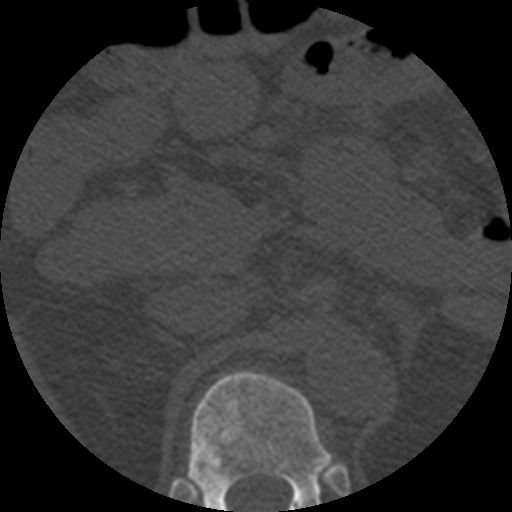
CT including the spine, one axial slice. Position 218 of 508 along the scan axis. 120 kVp. Bone window (W 1800 / L 400 HU). 1.25 mm slice thickness. 512 × 512 image matrix, field of view 160 × 160 mm. Patient age 57 years. From the clinical record (not read from this slice): primary cancer: prostate.
Outlined on this slice (semi-automatic segmentation, software-assisted and operator-edited):
- T12 vertebra: bounding box (x1, y1, x2, y2) in pixels: (187, 370, 336, 512)